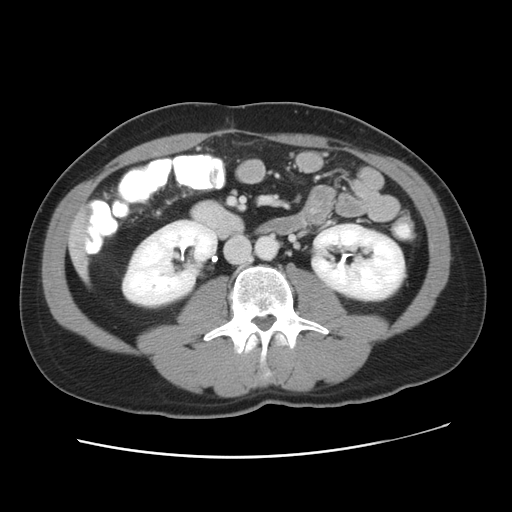
Contrast-enhanced abdominal CT, one axial slice. Slice 14 of 49 in the series (ordered by position). Reconstruction kernel STANDARD. 120 kVp. Soft-tissue window (W 400 / L 40 HU). 512 × 512 image matrix, field of view 363 × 363 mm. Male patient, age 41 years. From the clinical record (not read from this slice): diagnosis: colorectal cancer liver metastases, imaged before liver resection; multiple liver metastases: yes; largest metastasis: 0.7 cm; disease in both lobes: yes.
Structures marked on this image (outlined manually by an expert reader):
- liver: bounding box <70,214,86,272> (left, top, right, bottom; pixels)